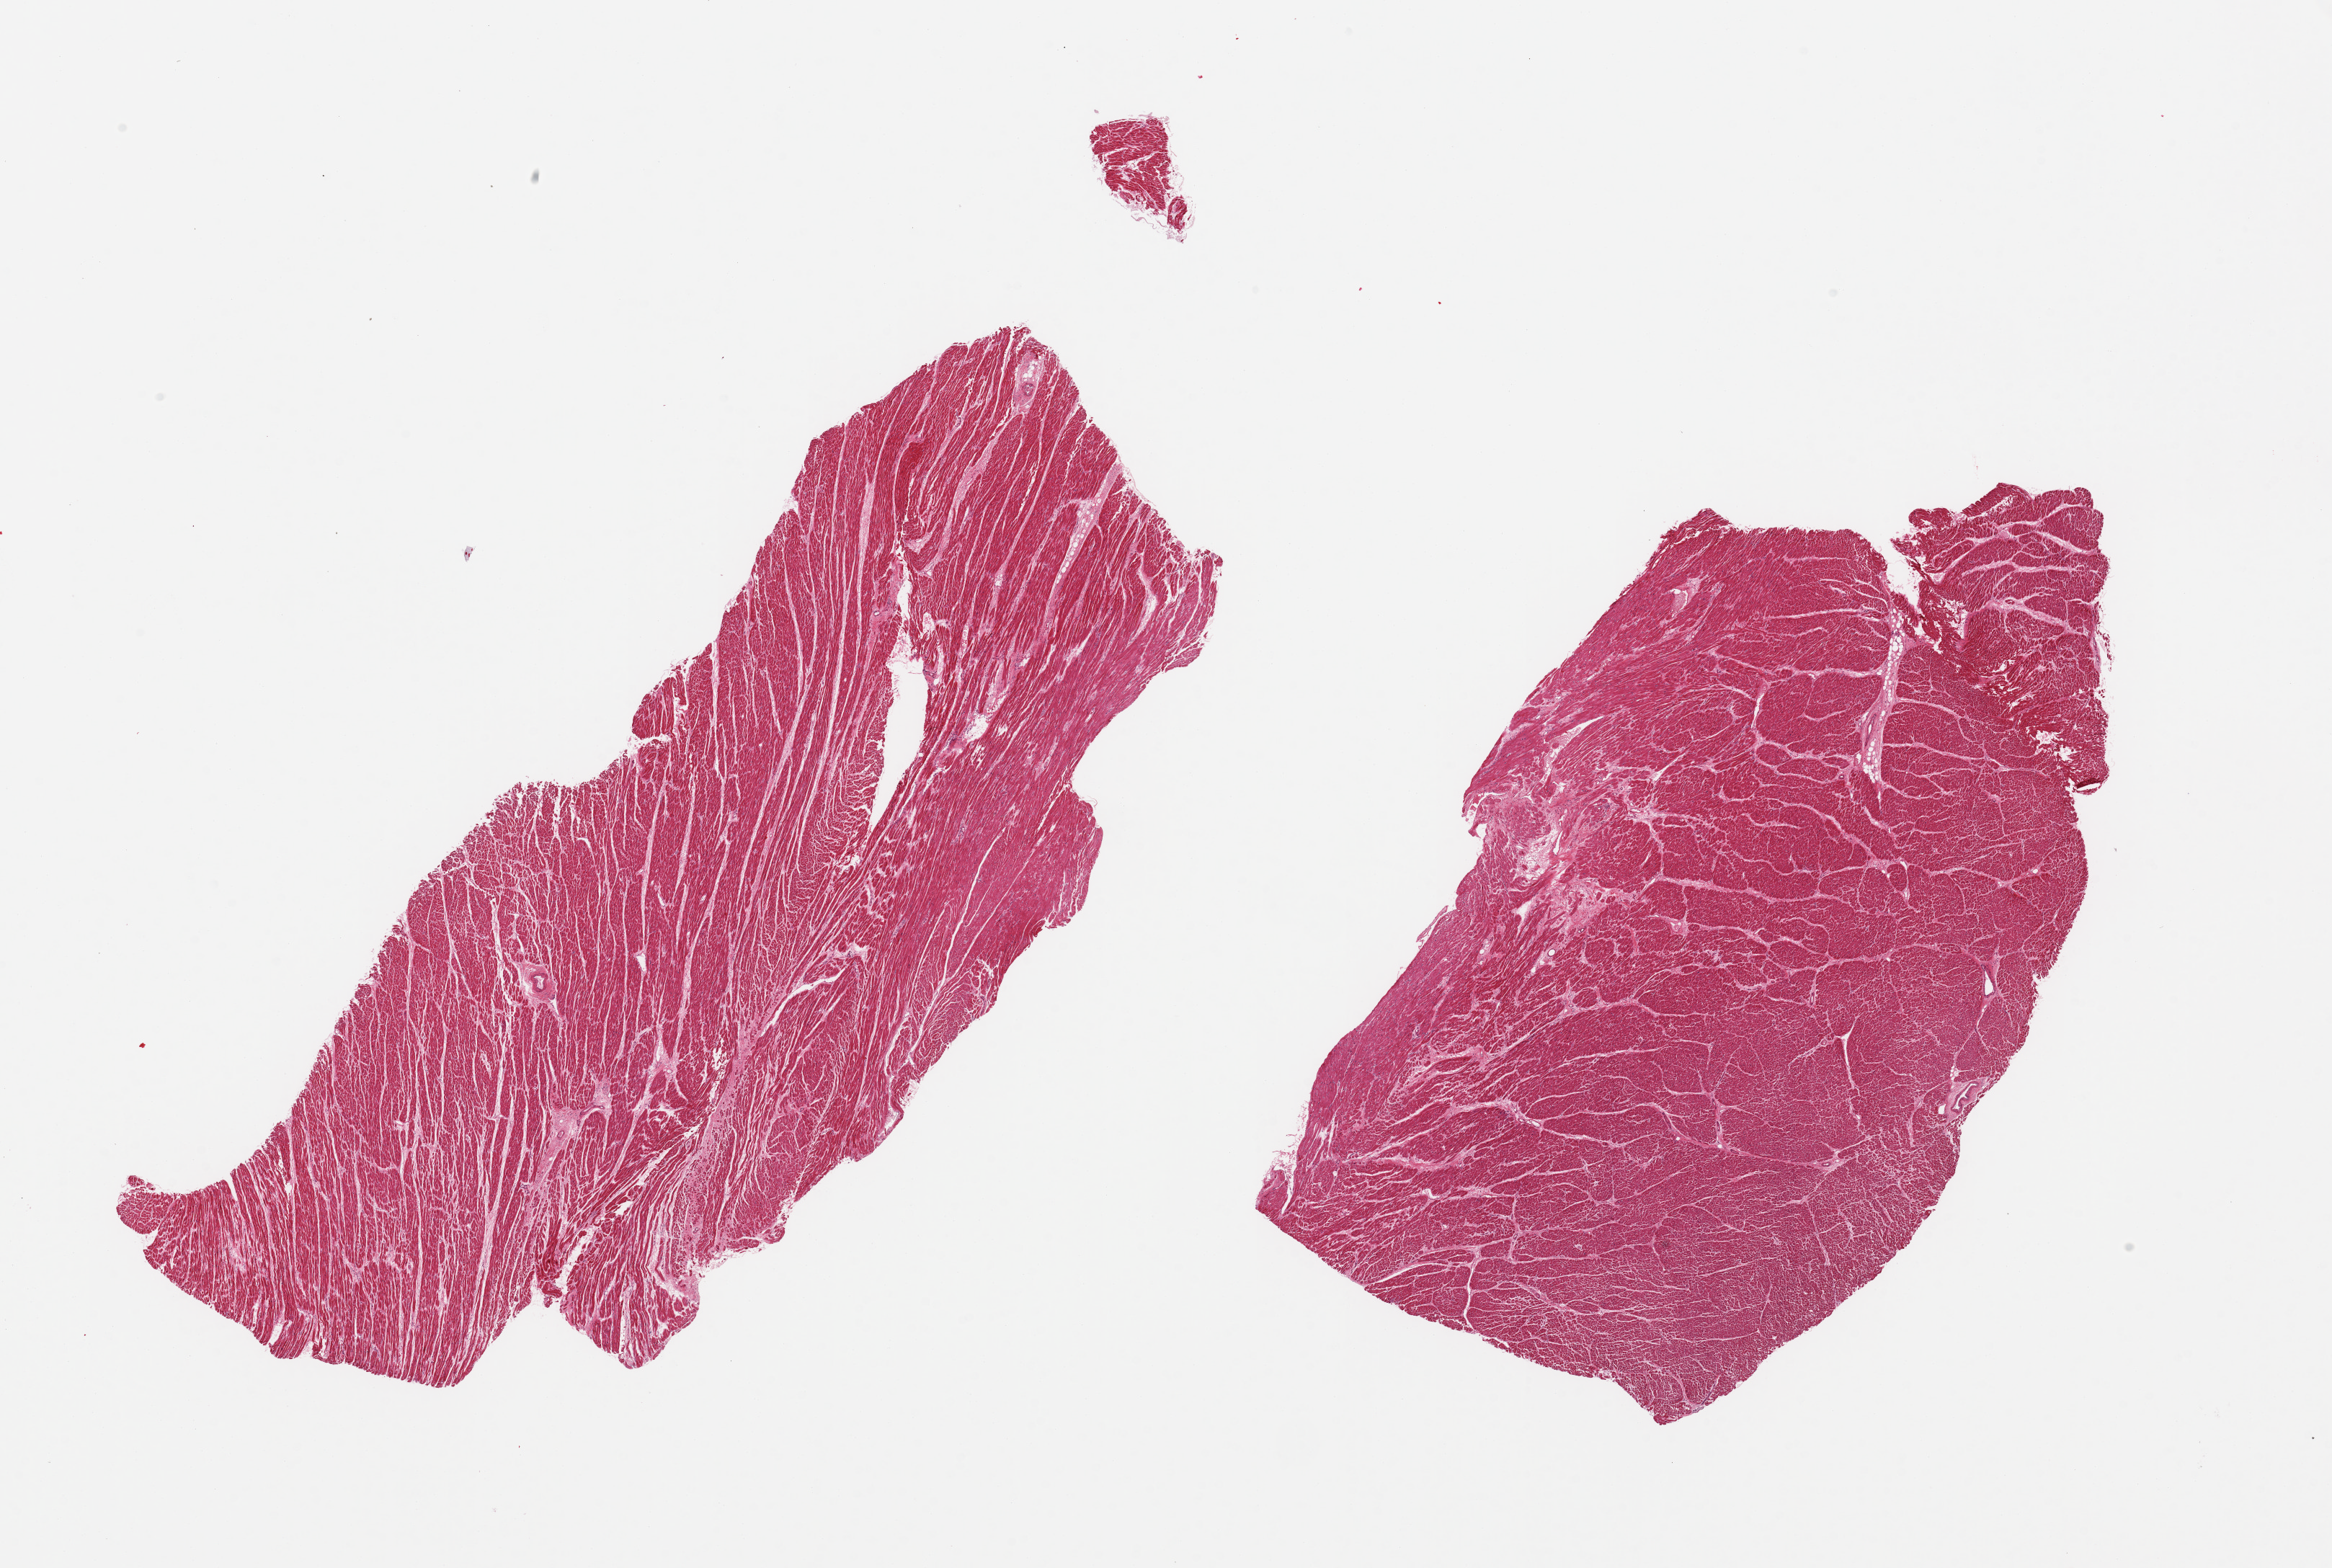
Digitized H&E-stained section, brightfield — shown as a low-resolution overview of the whole scanned area (about 25.6 x 17.2 mm); PAXgene-fixed paraffin-embedded (PFPE) section; sampled site (target tissue): heart; tissue donor sample. Male donor.
Reviewer comment on this tissue sample: 2 pieces; interstitial fibrosis and myocyte hypertrophy.